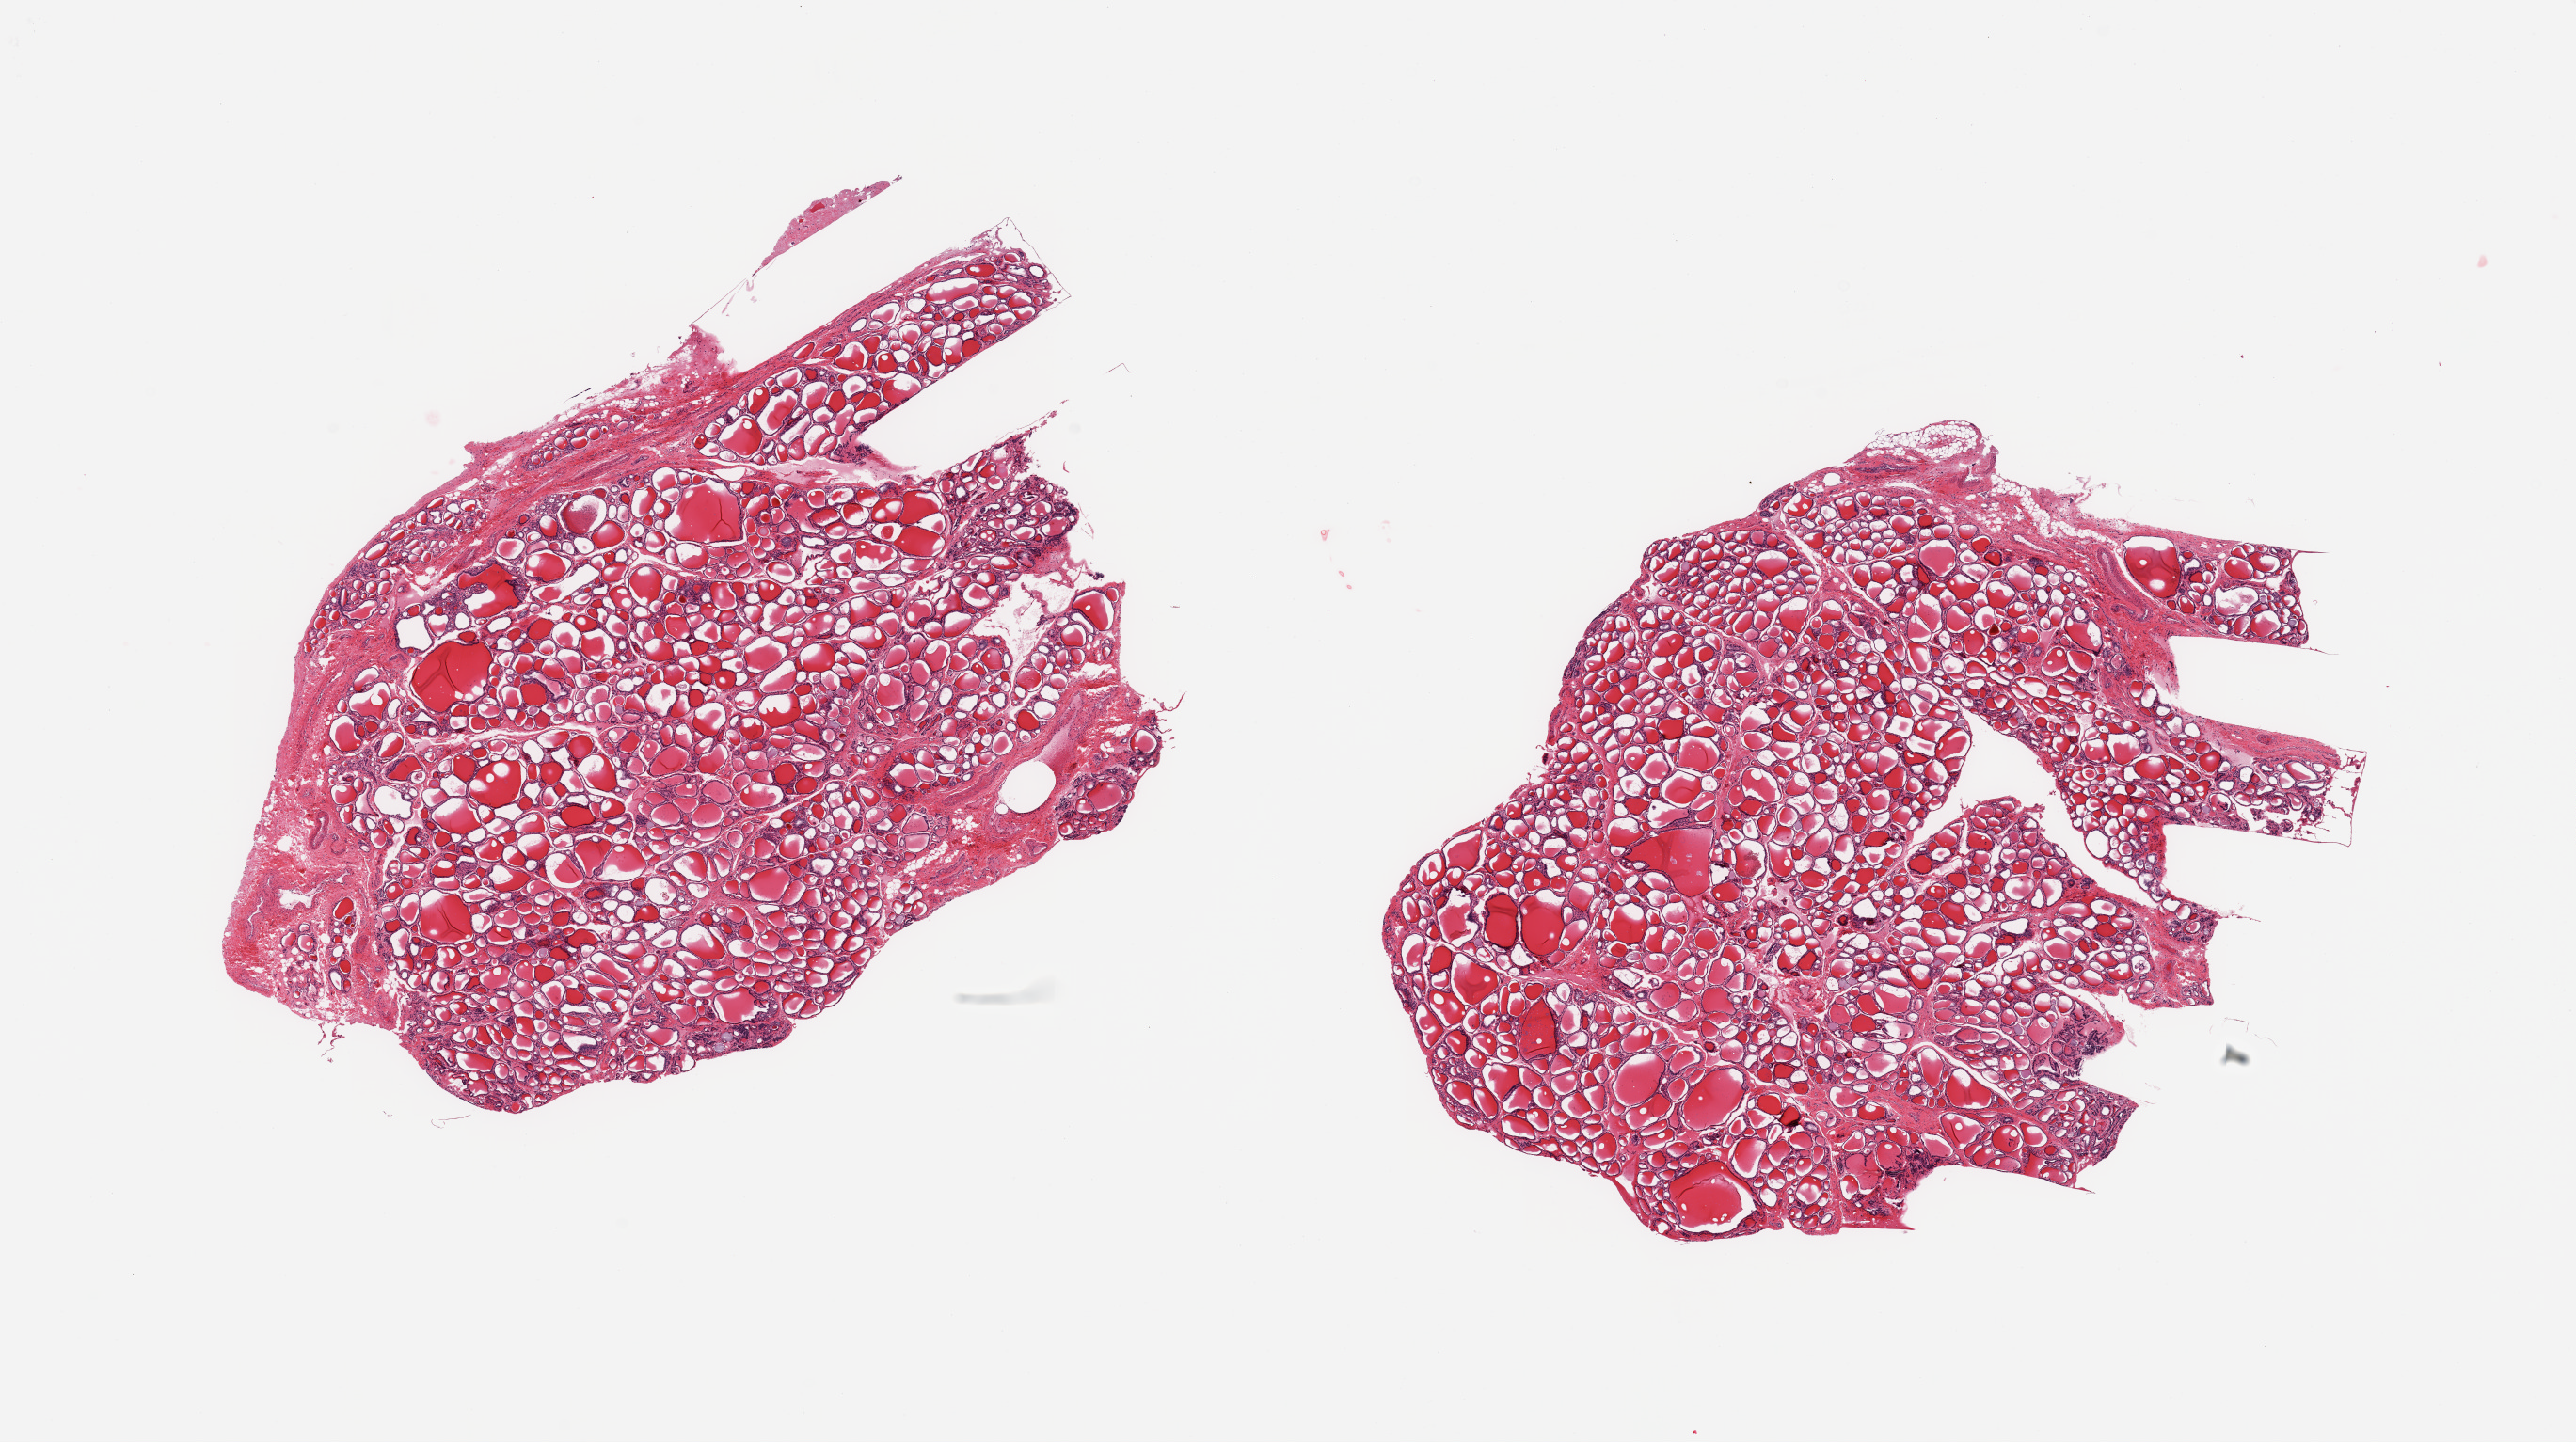
Haematoxylin and eosin whole-slide image, a low-resolution overview of the entire scanned area, about 21.7 x 12.1 mm, PAXgene-fixed, paraffin-embedded tissue, target tissue: thyroid, donor tissue sample. Donor: female.
- pathologist's review note for this sample: 2 pieces; no lesions